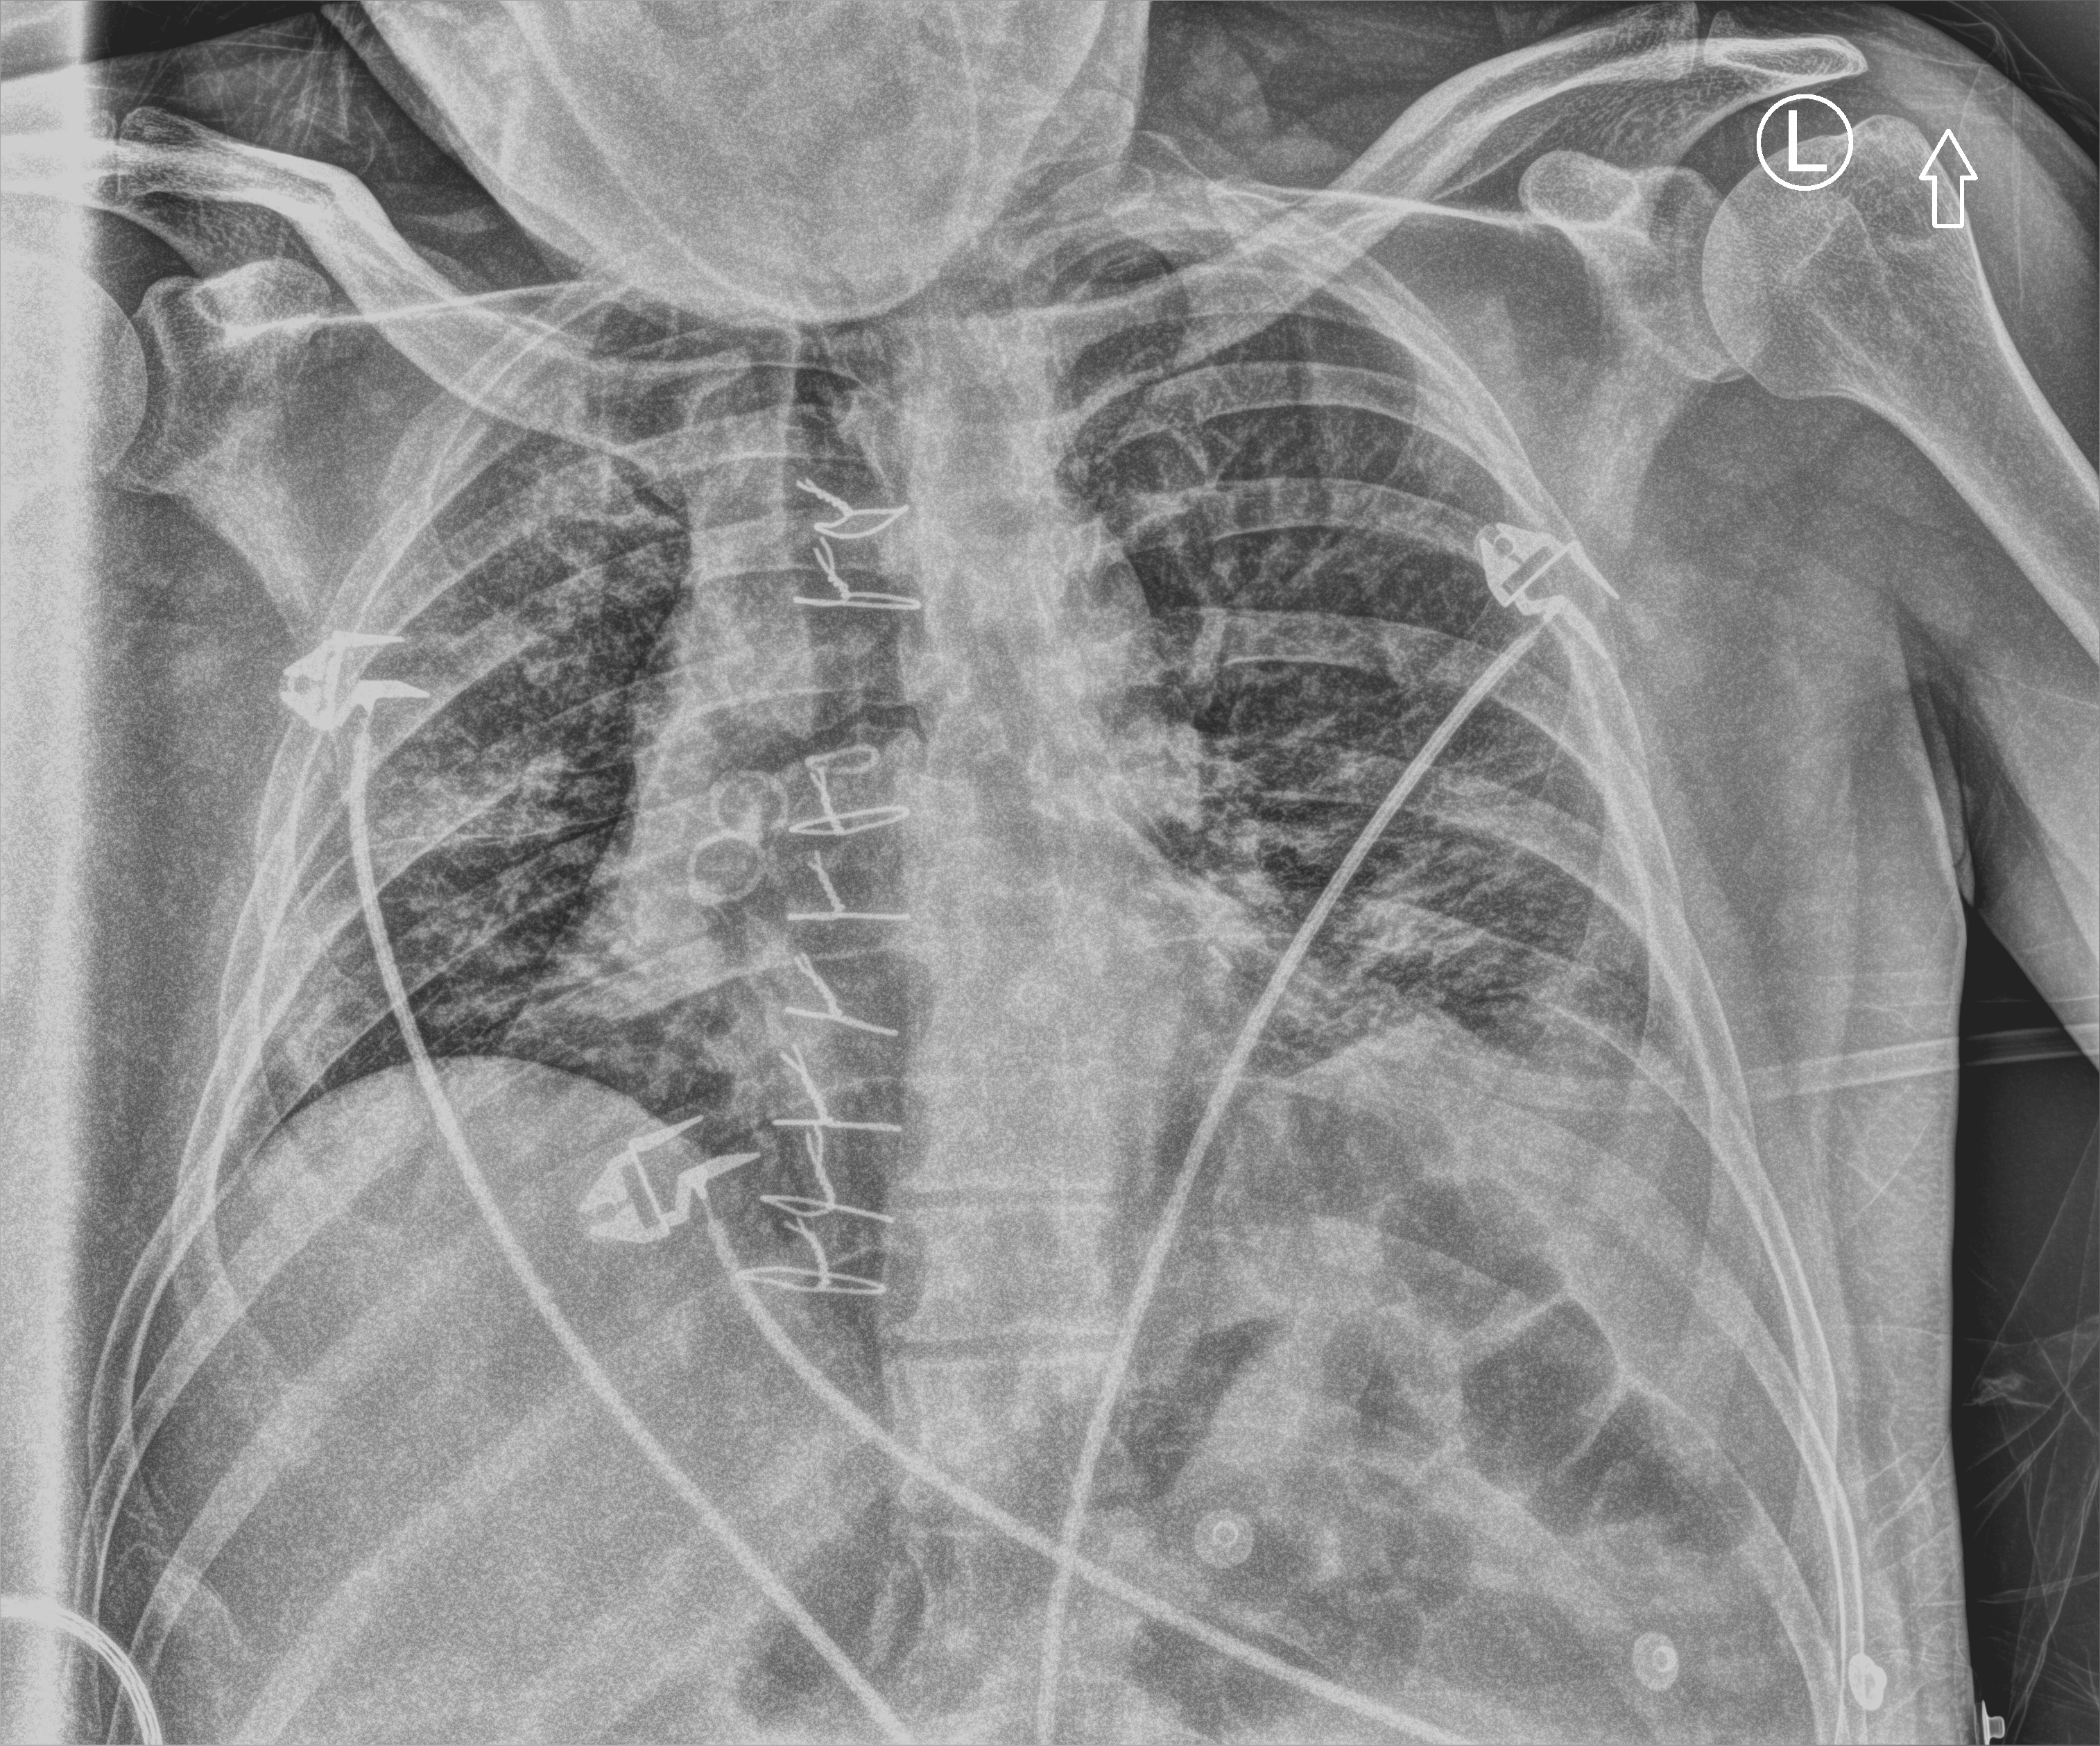
Portable chest radiograph; anteroposterior (AP) projection. Male patient hospitalised with COVID-19, age 18–59 years.
Admission-level facts for this patient (not findings on this image; timing relative to this image not recorded):
- mechanically ventilated during this hospital stay: yes